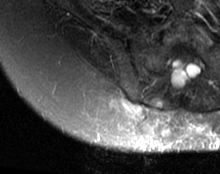
MRI of an extremity soft-tissue mass, one axial slice; position 47 of 63 along the scan axis; T2-weighted fat-saturated; MR volume resampled by the dataset authors to the PET/CT grid (not the native acquisition matrix); 3.27 mm slice thickness; 220 × 174 image matrix, field of view 215 × 170 mm. Female patient. Case-level facts recorded for this patient, not image findings: histological type: spindle cell suggestive of myxofibrosarcoma; grade: intermediate; site of the primary tumour: right buttock.
Outlined on this slice (expert contour drawn on MRI and transferred to this co-registered scan by the dataset authors):
- gross tumour volume (mass): box from (x=116, y=97) to (x=174, y=137) px